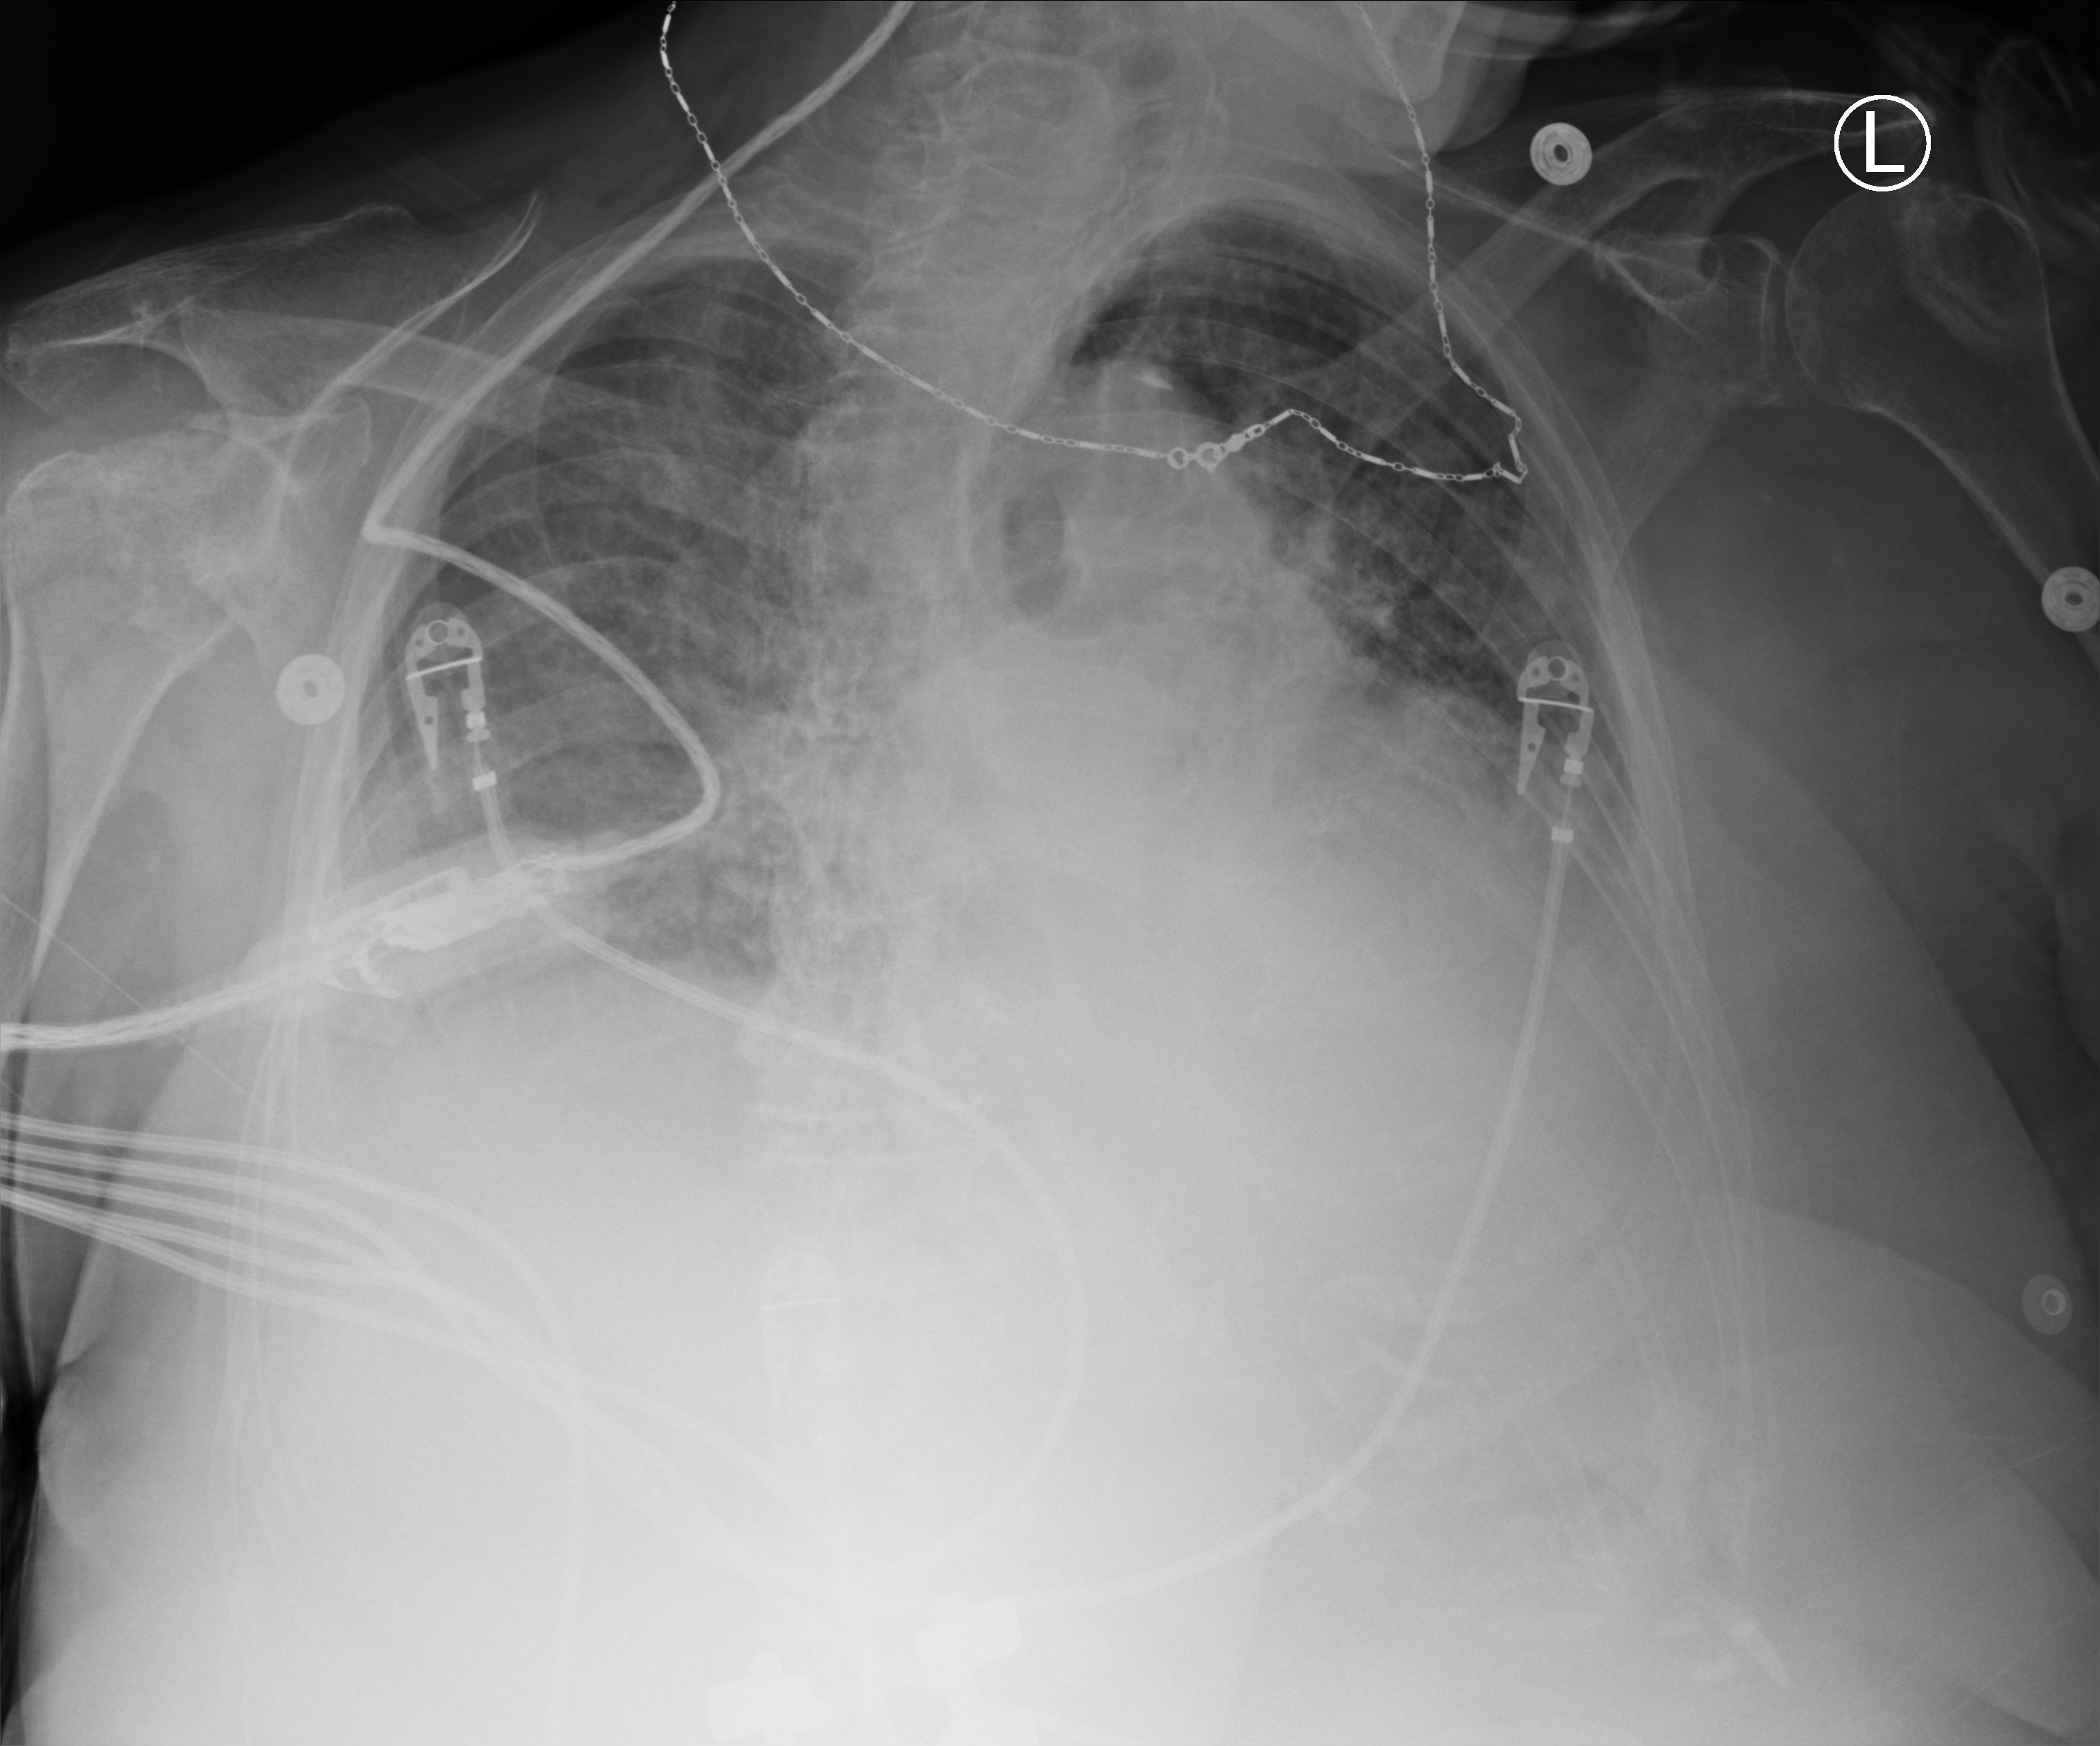
Portable chest radiograph. Patient hospitalised with COVID-19; female, aged 75–90 years.
Hospital-stay facts (about this admission, not read from this image; timing relative to this image not recorded):
- admitted to intensive care during this hospital stay: no
- mechanically ventilated during this hospital stay: no
- other chronic lung disease (admission record): no